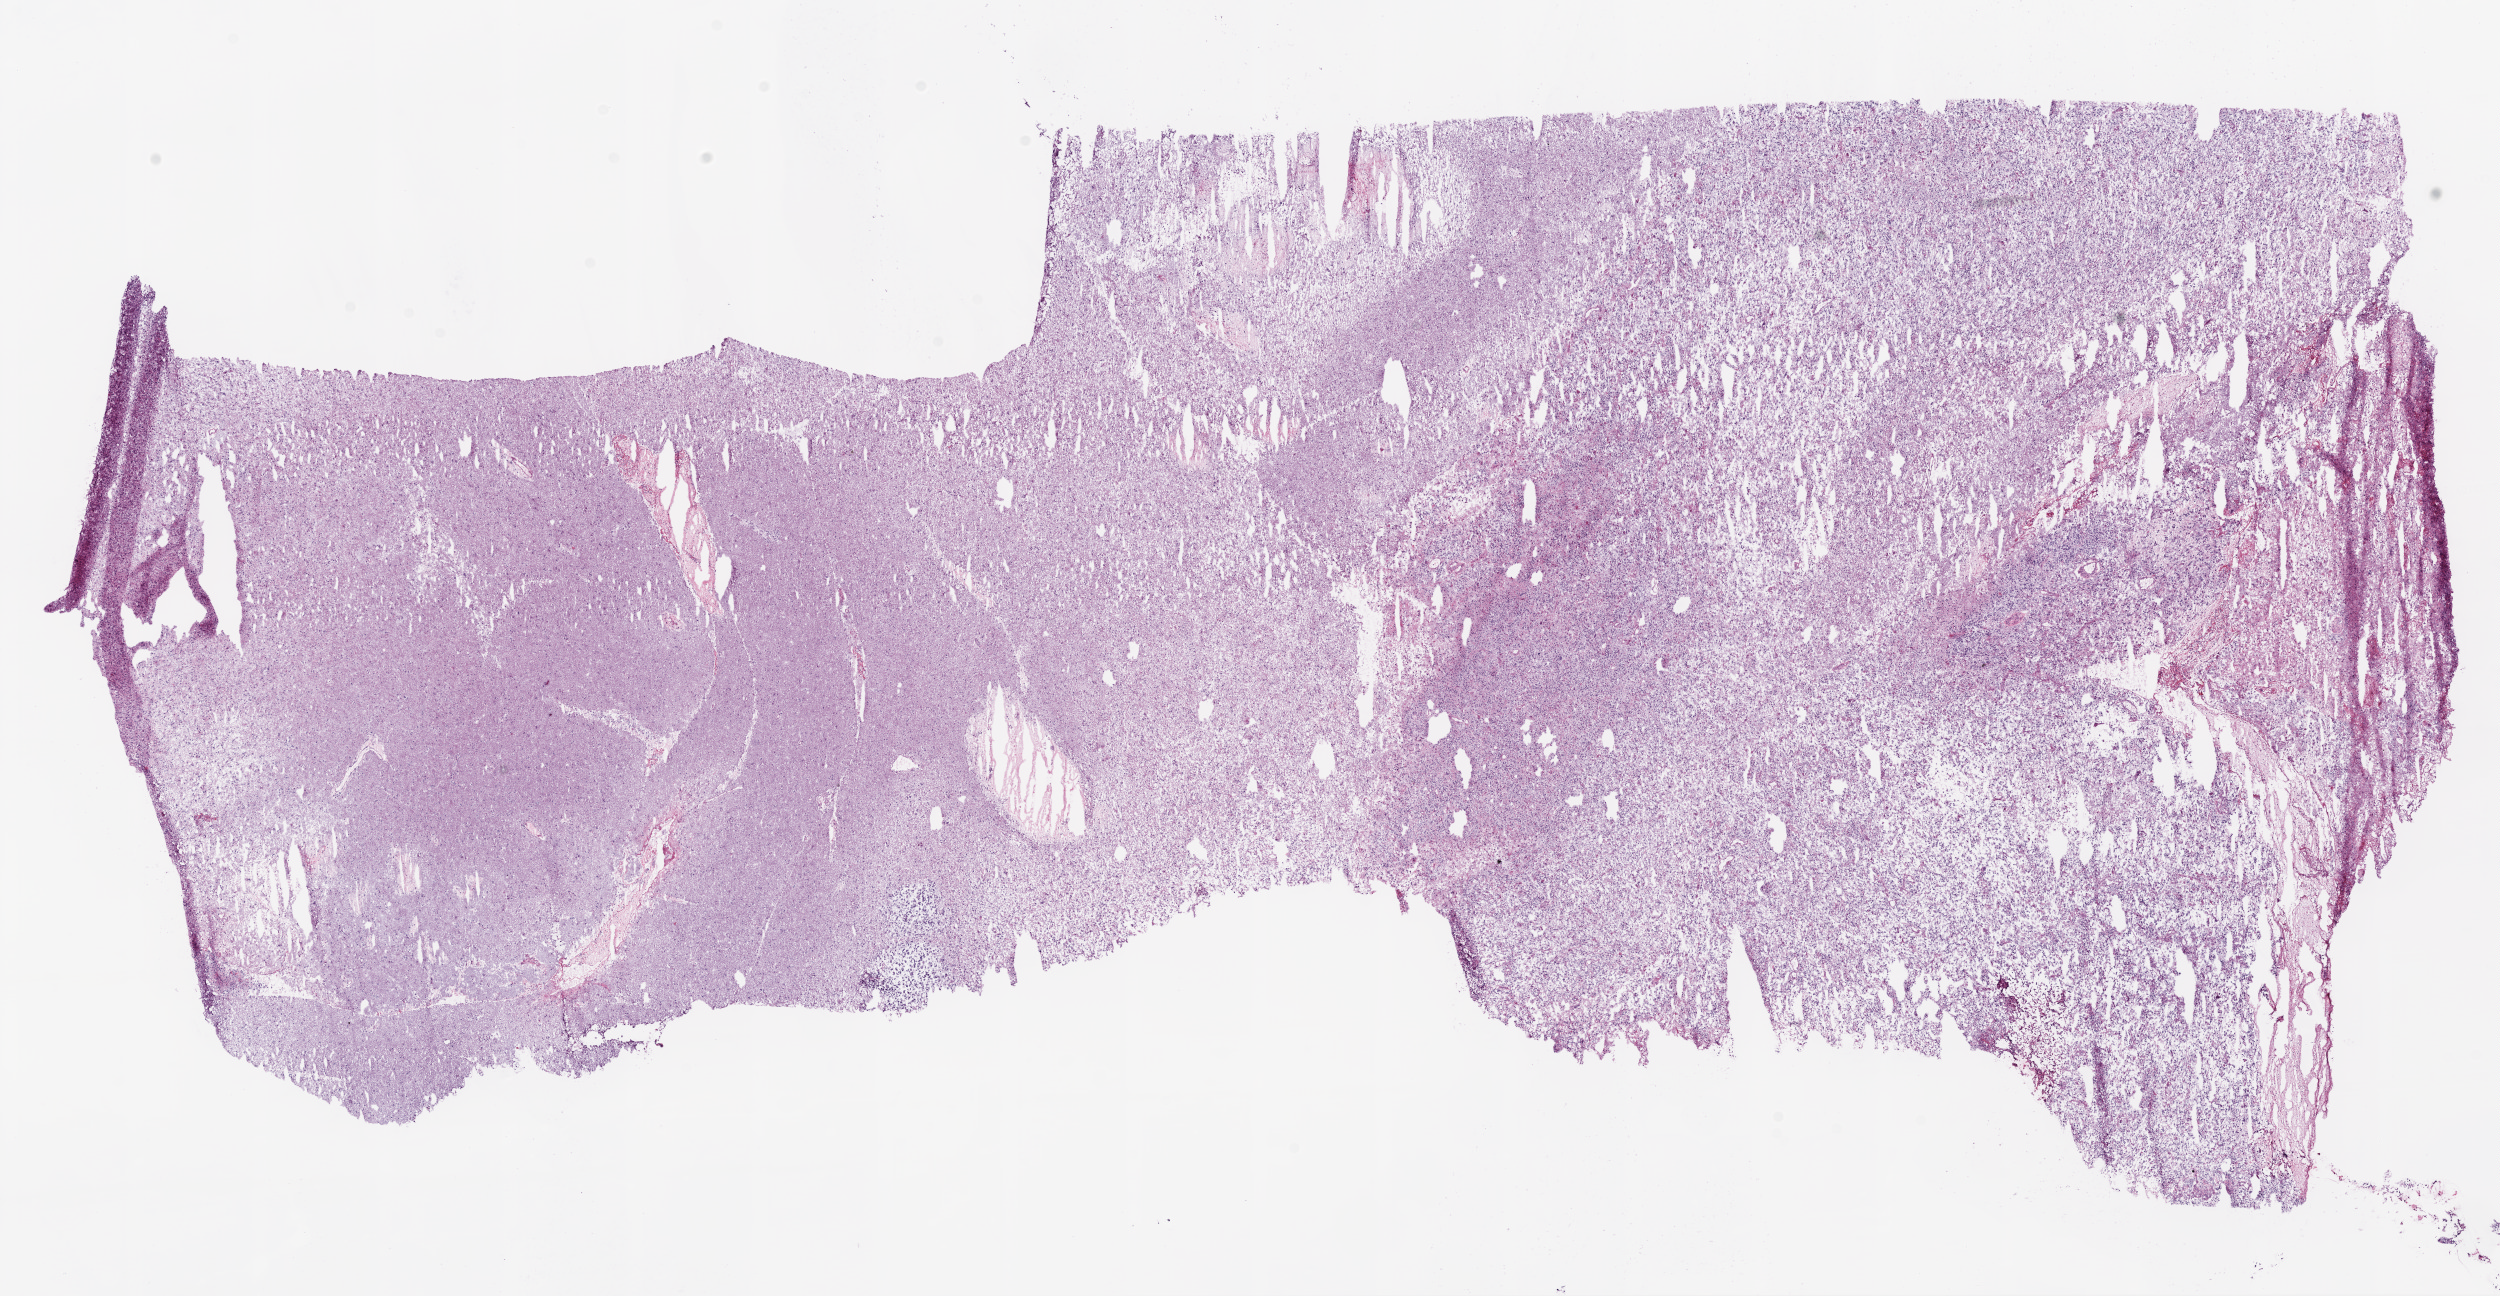
Whole-slide histology image, H&E, low-resolution overview of the scanned area, about 20.1 x 10.4 mm; frozen section from the bottom of the tissue portion; sample: primary tumour, brain. Male, age 59 years at initial diagnosis. Slide review estimates, as recorded: tumour cells 95%, tumour nuclei 80%, normal cells 0%, stromal cells 0%, necrosis 5%.
Histologic diagnosis: Glioblastoma.